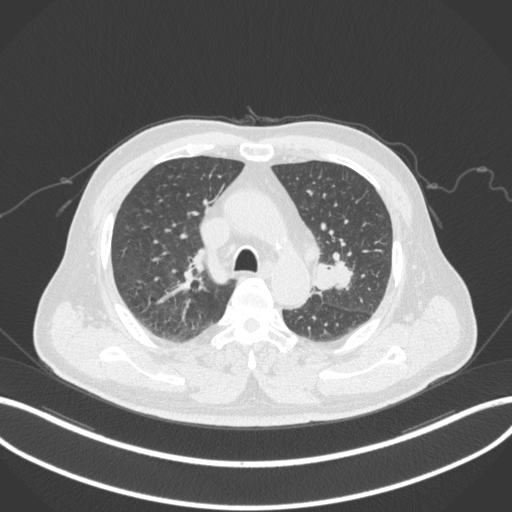
Chest CT, one axial slice; slice 206 of 286 in the series (ordered by position); reconstruction kernel B31f; lung window (W 1500 / L -600 HU); 512 × 512 image matrix, field of view 400 × 400 mm. Male patient, age 67 years. From the clinical record (not read from this slice): clinical TNM (as recorded): T2a N1 M0; histopathological grade: G3.
Annotated regions visible in this slice (bounding box drawn by a radiologist):
- lung tumour (recorded histology: adenocarcinoma): box from (x=314, y=253) to (x=354, y=292) px